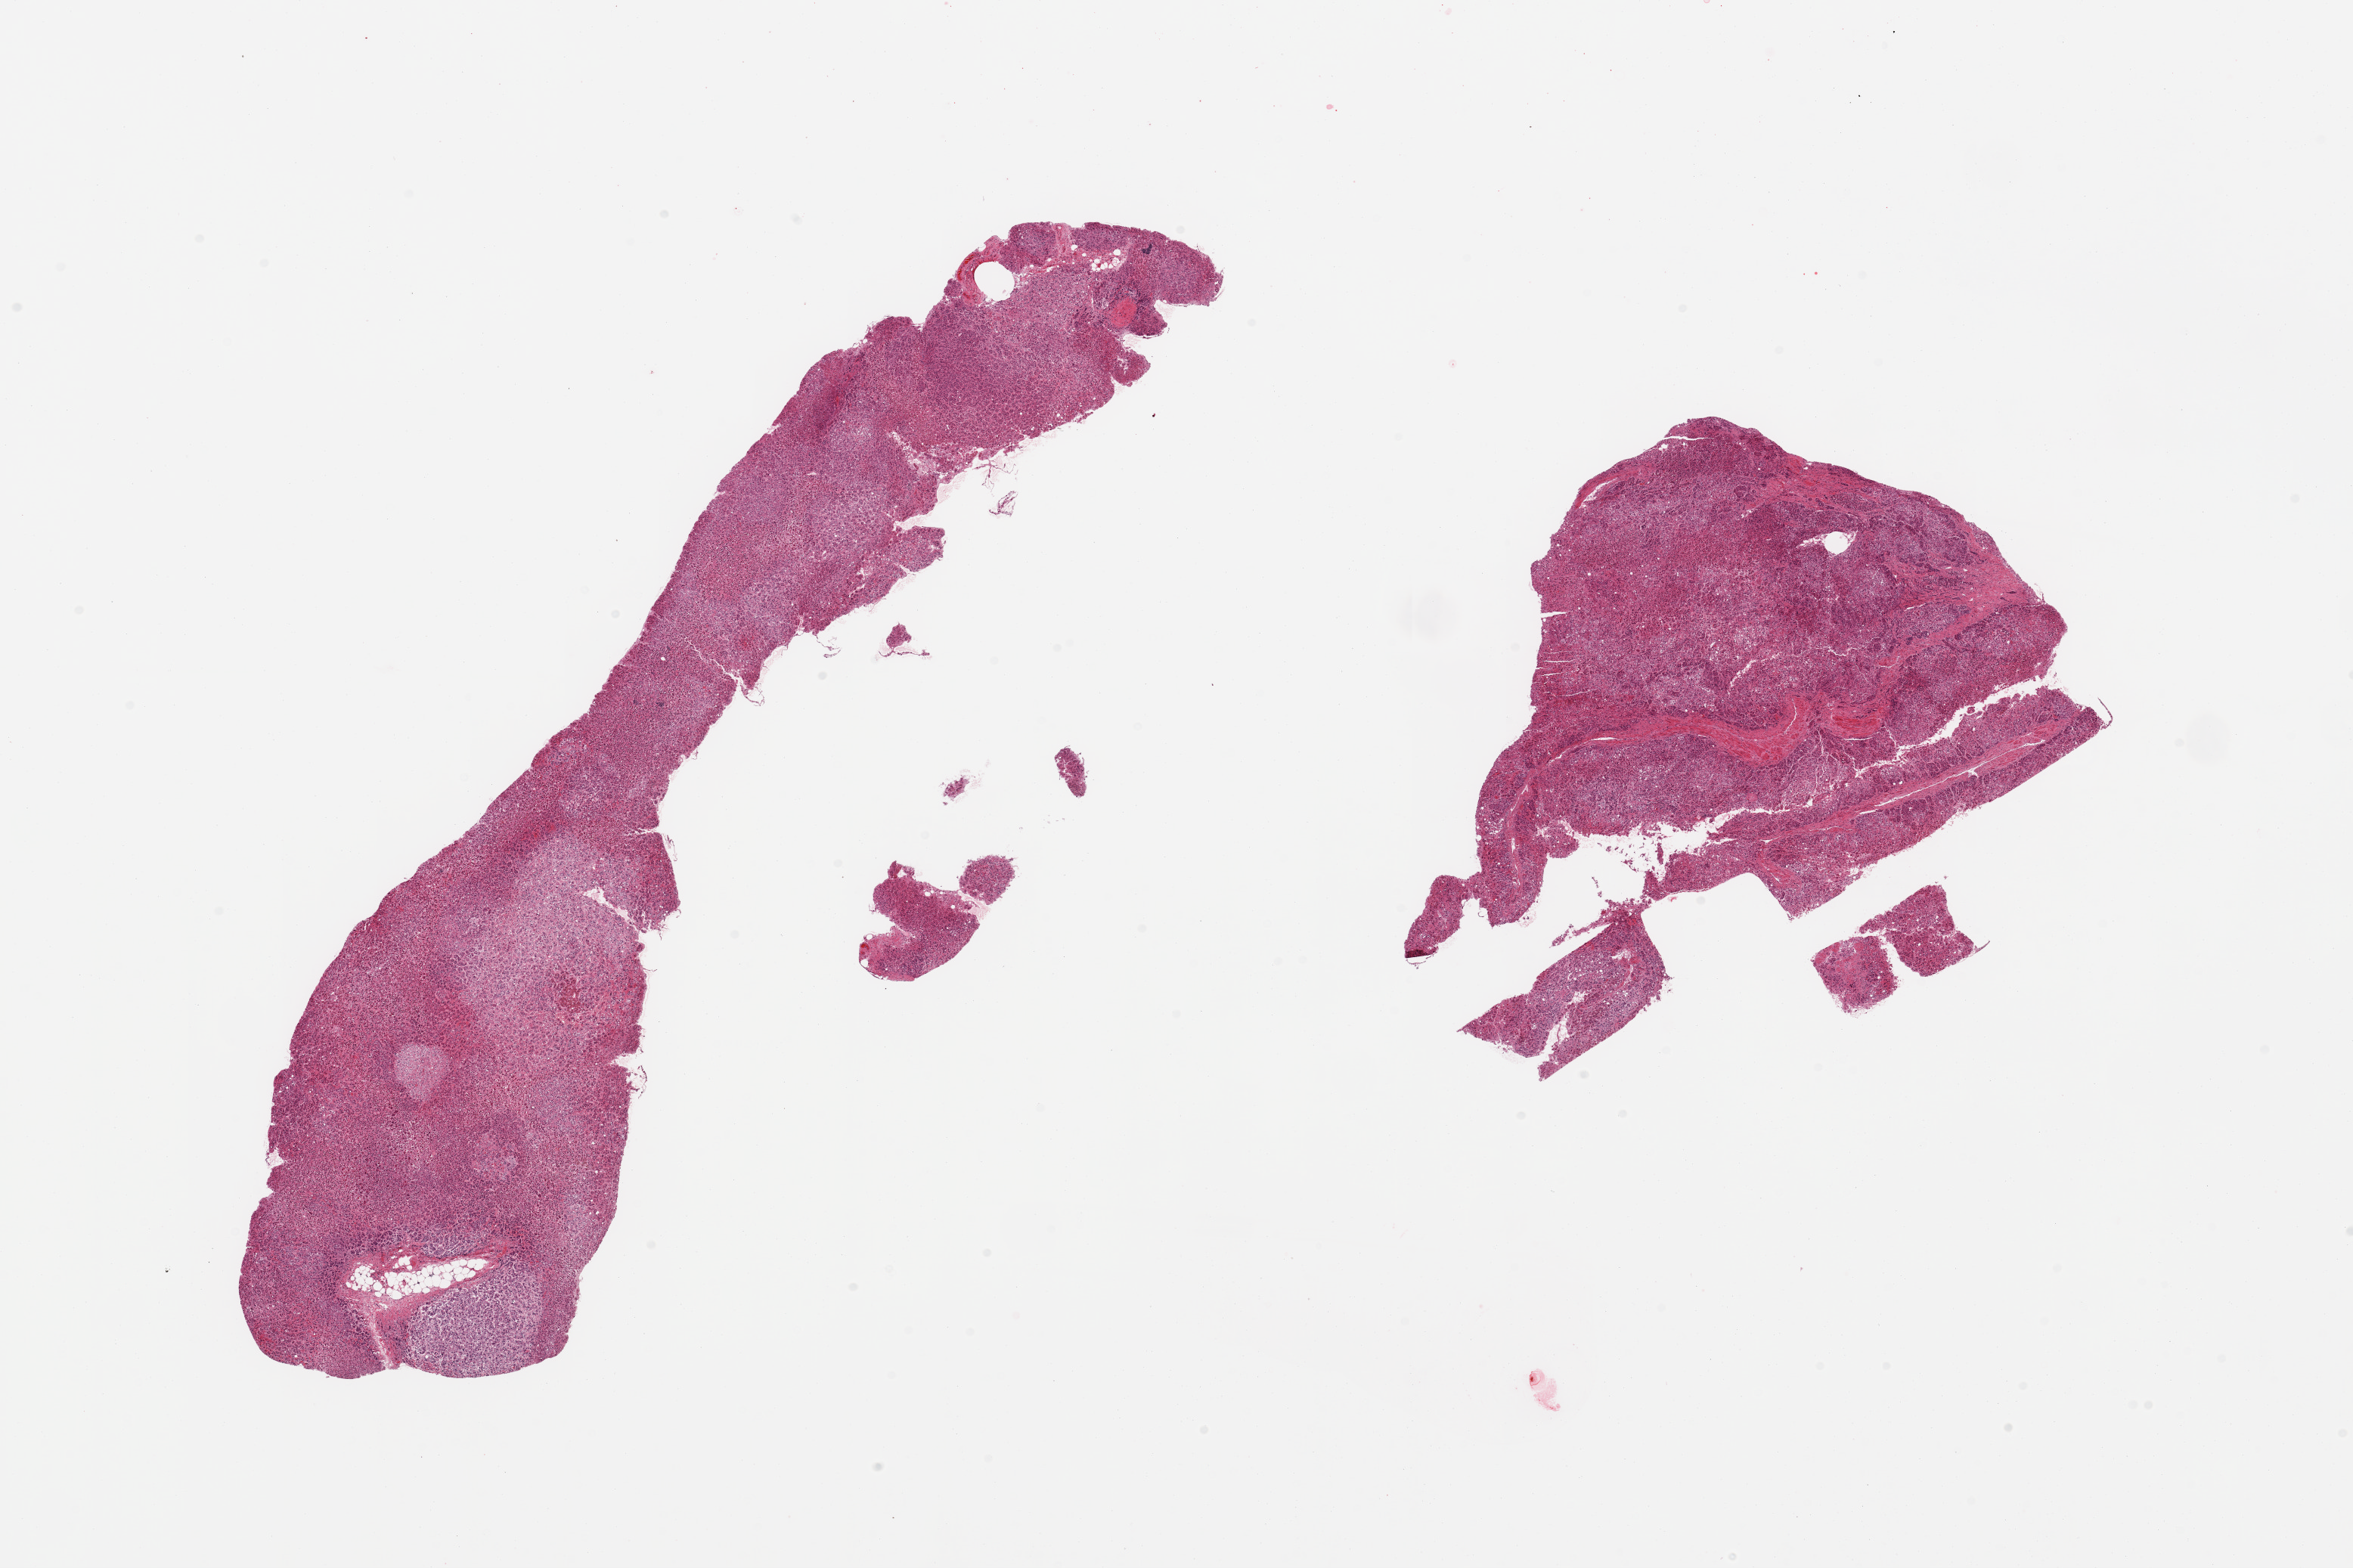
Whole-slide image, hematoxylin and eosin (H&E) stain, brightfield — whole scanned area (about 24.6 x 16.4 mm, from a 20x scan) shown as a low-resolution overview, PAXgene-fixed, paraffin-embedded tissue, section of adrenal gland (target tissue), donor tissue sample. Donor sex: female.
Review note (as recorded): 2 fragmented pieces.